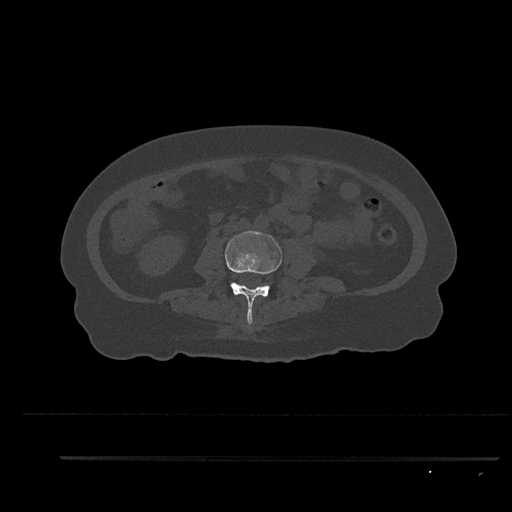
CT including the spine, one axial slice. Position 77 of 797 along the scan axis. Reconstruction kernel Br40s/3. Bone window (W 1800 / L 400 HU). 0.5 mm slice thickness. 512 × 512 image matrix, field of view 408 × 408 mm. Patient: female, 44 years. From the clinical record (not read from this slice): primary cancer: renal; vertebrae with lytic lesions (as recorded): L1.
Annotated regions visible in this slice (semi-automatically segmented with operator editing):
- L3 vertebra: box from (x=225, y=231) to (x=282, y=324) px